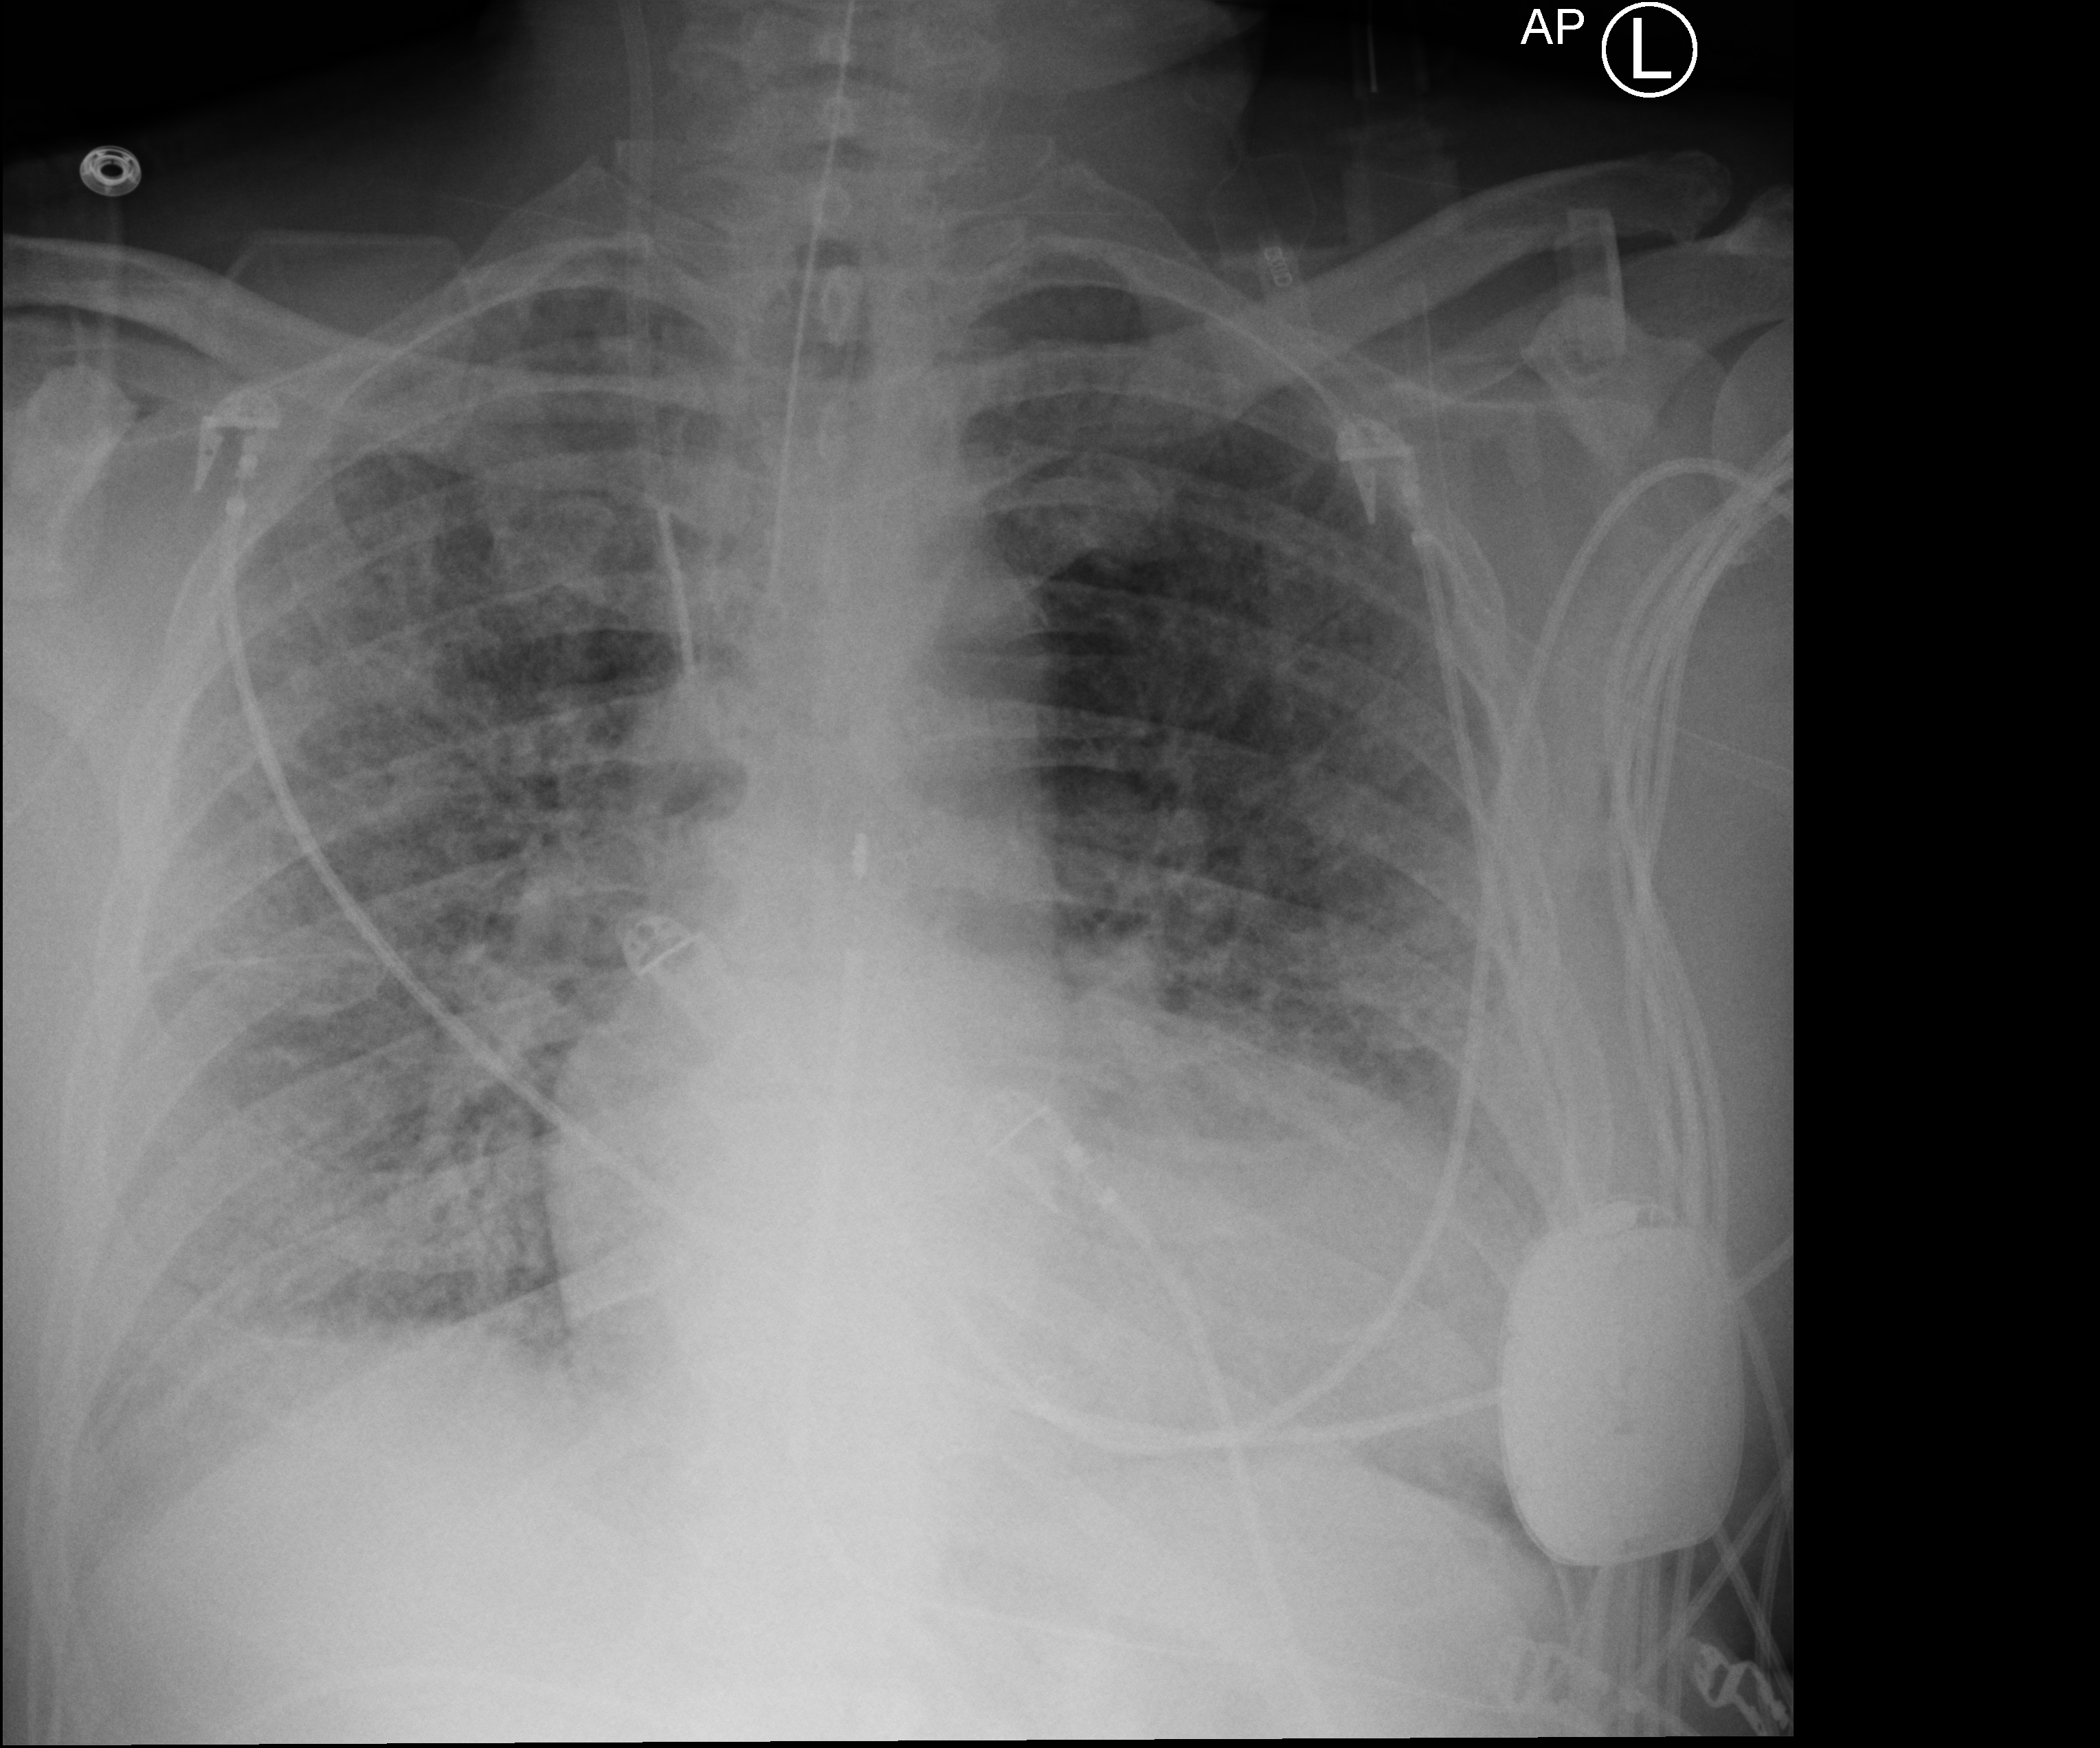
Bedside chest radiograph (computed radiography), anteroposterior (AP) projection. Patient hospitalised with COVID-19; male, aged 60–74 years.
From the hospital-stay record, not from the radiograph (when in the stay this image was taken is not recorded):
- length of hospital stay: 16 days
- other chronic lung disease (admission record): no